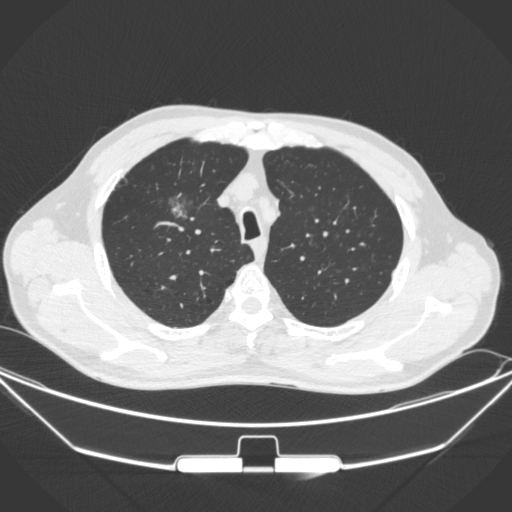
Chest CT, one axial slice; position 271 of 355 along the scan axis; 120 kVp; lung window (W 1500 / L -600 HU); 1 mm slice thickness; 512 × 512 image matrix, field of view 399 × 399 mm. Male patient, age 67 years. From the clinical record (not read from this slice): clinical TNM (as recorded): T1c N0 M0; histopathological grade: G2.
Structures marked on this image (rectangle marked by the reading radiologist):
- lung tumour (recorded histology: adenocarcinoma): bounding box (x1, y1, x2, y2) in pixels: (156, 195, 197, 232)